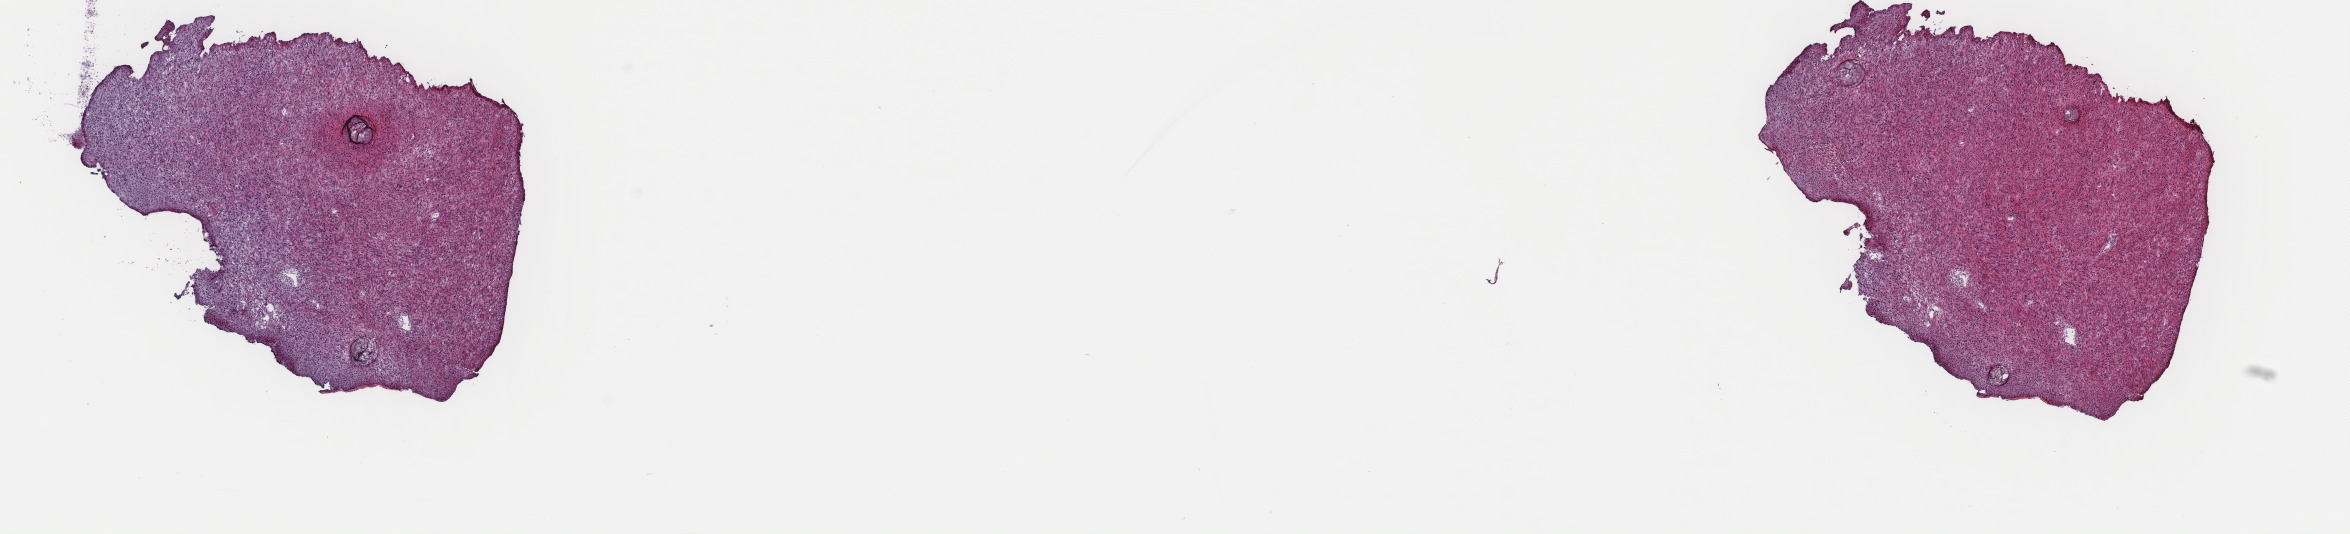
Digitized H&E tissue section (whole slide) — whole scanned area (about 18.7 x 4.2 mm) shown as a low-resolution overview, frozen section from the top of the tissue portion, primary tumour sample from the connective, subcutaneous and other soft tissues. Patient: male, age at initial diagnosis 42 years. Slide review estimates, as recorded: tumour cells 100%, tumour nuclei 95%, normal cells 0%, stromal cells 0%, necrosis 0%. Infiltration values recorded for this section: lymphocyte infiltration 1%, monocyte infiltration 0%, neutrophil infiltration 0%.
• diagnosis: Leiomyosarcoma, NOS (connective, subcutaneous and other soft tissues of lower limb and hip)